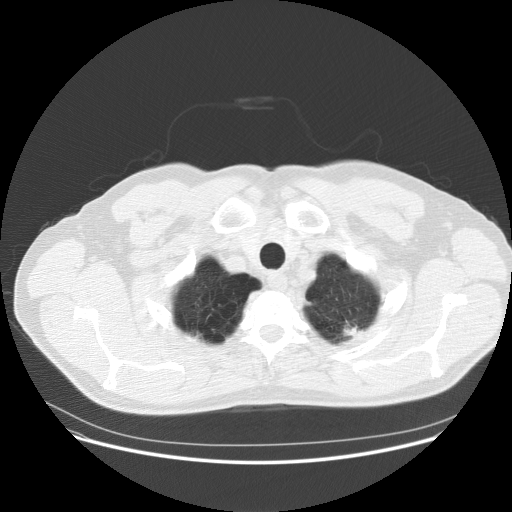
Low-dose screening chest CT, one axial slice. Slice 150 of 158 in the series (ordered by position). 120 kVp. Lung window (W 1500 / L -600 HU). 2.5 mm slice thickness. 512 × 512 image matrix.
Annotated regions visible in this slice (manually delineated by an expert):
- lesion 1 (tumor, upper lobe of left lung): box from (x=343, y=321) to (x=364, y=336) px